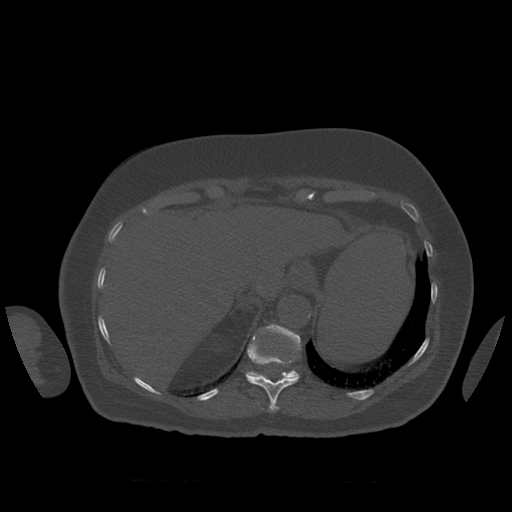
CT including the spine, one axial slice; slice 316 of 399 in the series (ordered by position); bone window (W 1800 / L 400 HU); 1.25 mm slice thickness; 512 × 512 image matrix, field of view 404 × 404 mm. Patient age 81 years. From the clinical record (not read from this slice): primary cancer: renal; vertebrae with lytic lesions (as recorded): L1.
Structures marked on this image (semi-automatic segmentation, software-assisted and operator-edited):
- T11 vertebra: box from (x=247, y=336) to (x=299, y=412) px
- T12 vertebra: (x=246, y=324)–(x=301, y=379)